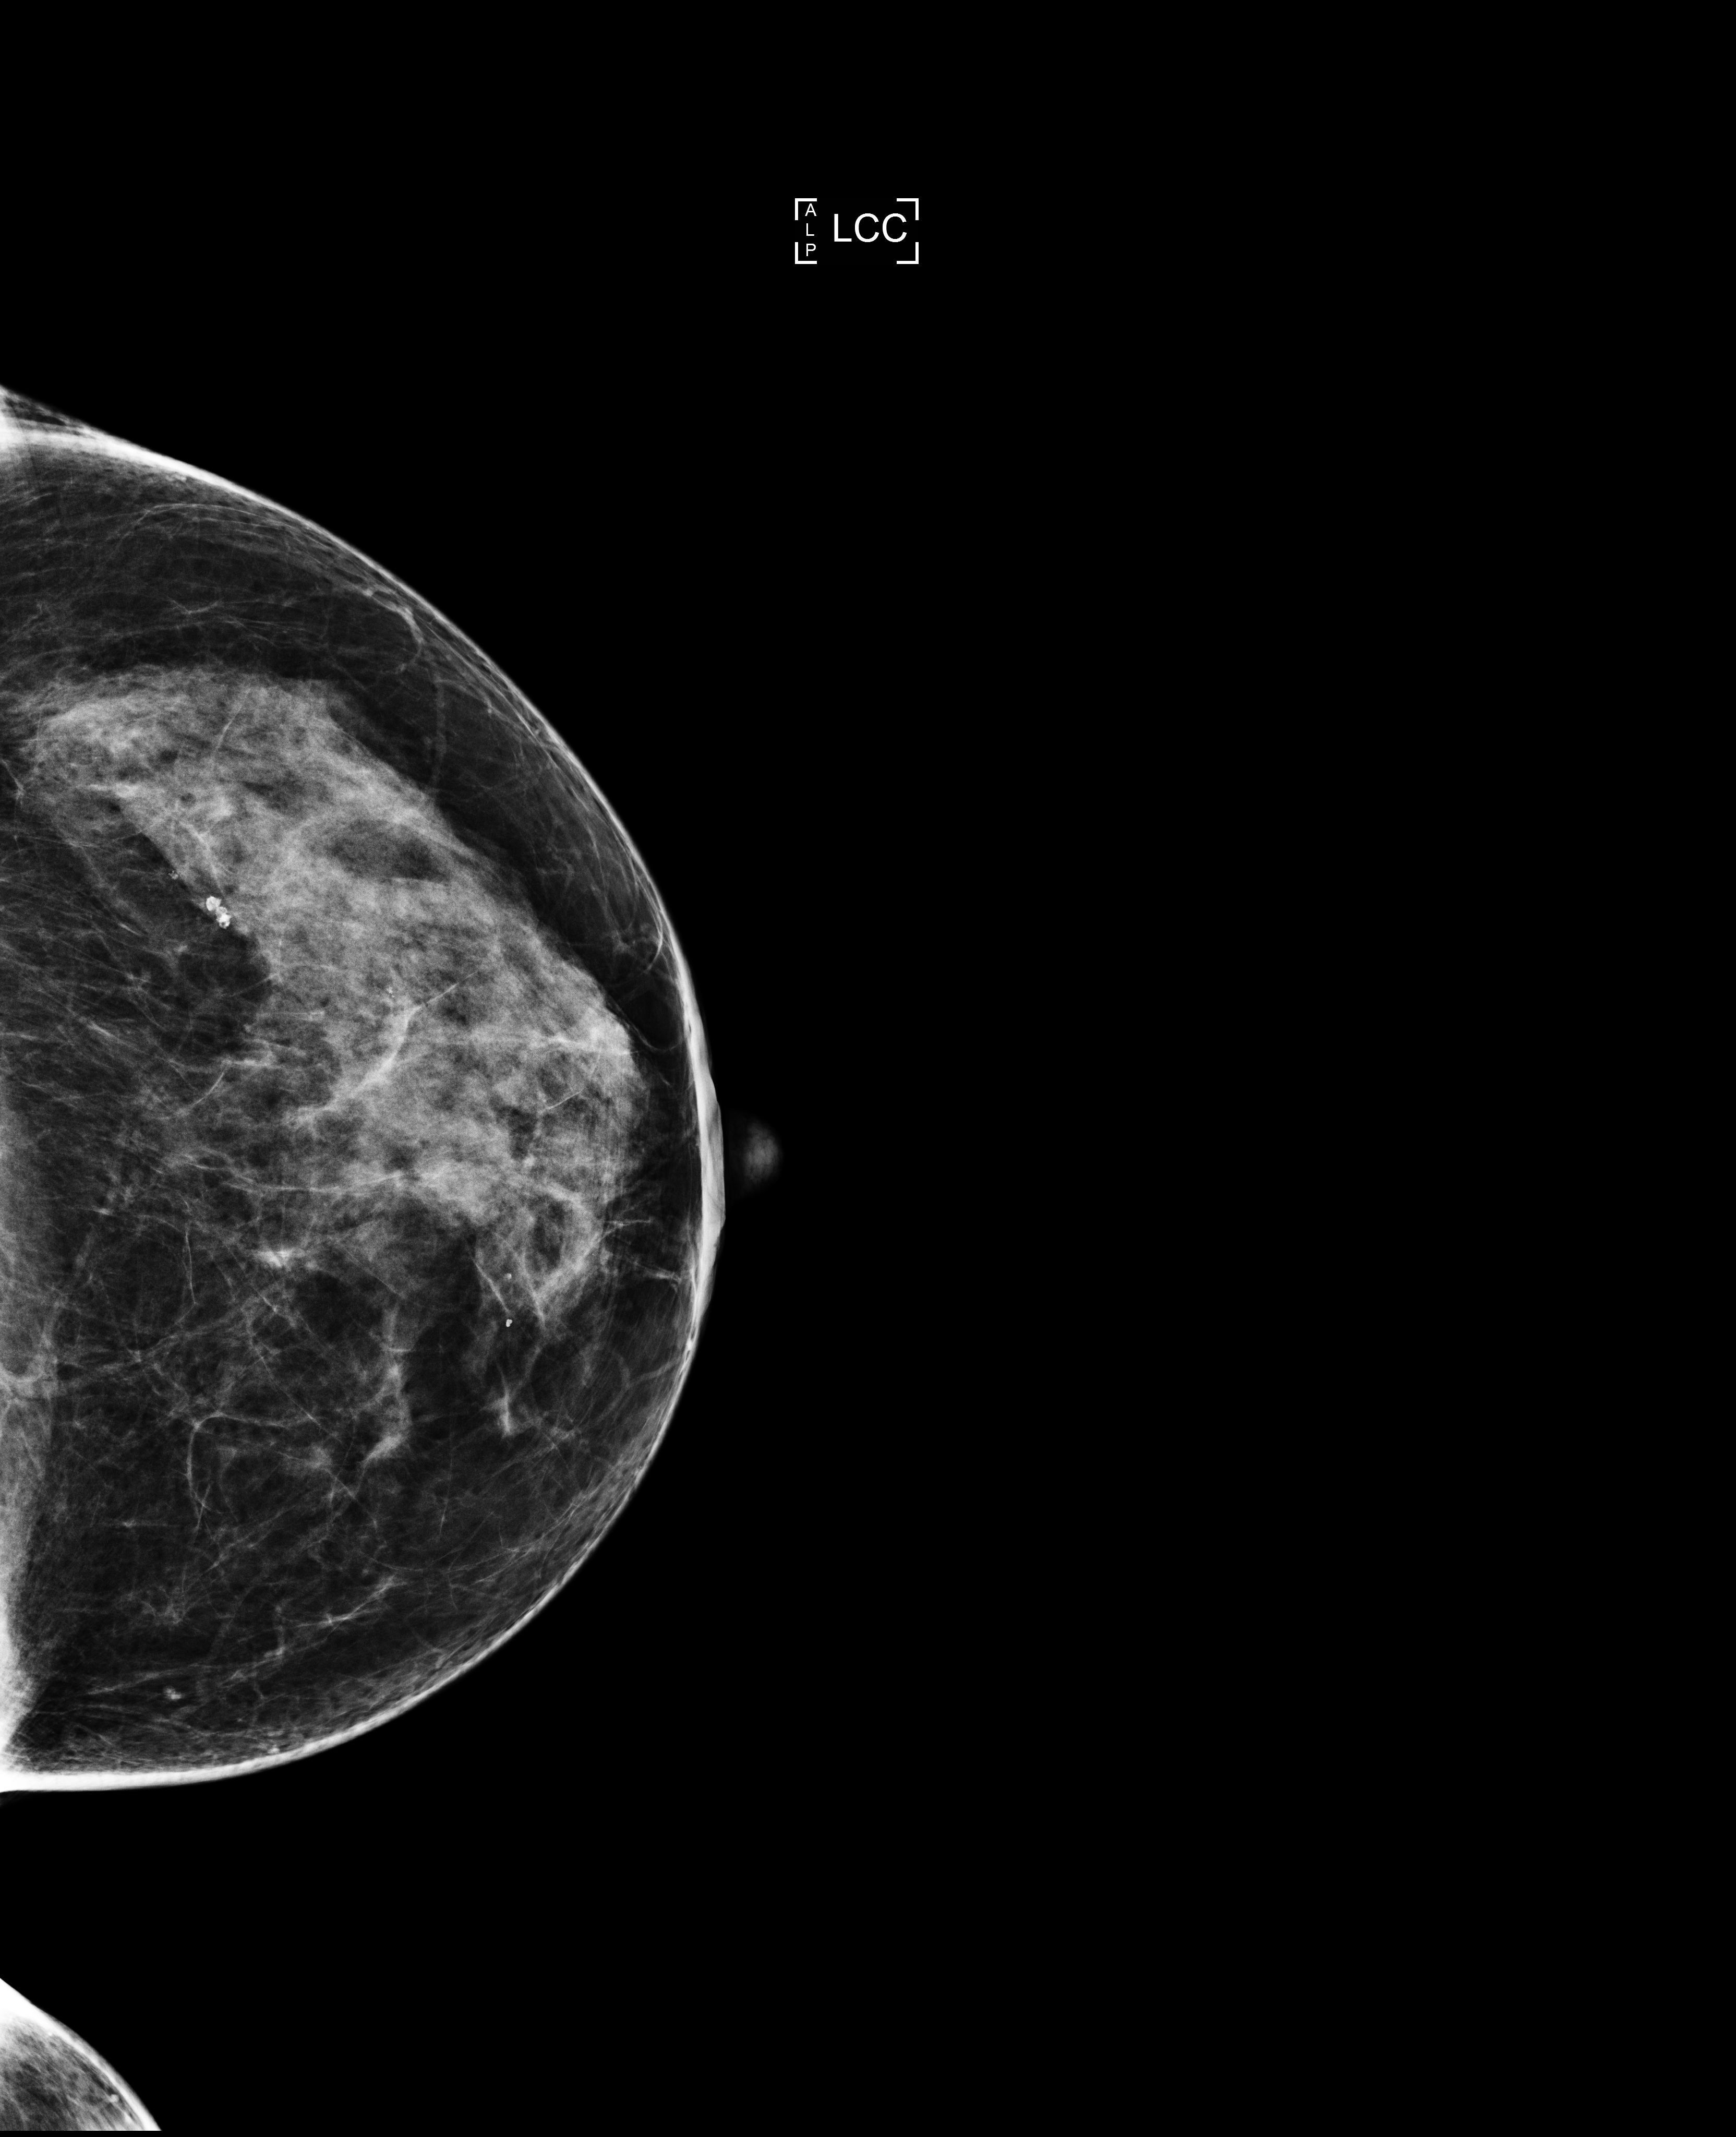
Full-field digital mammogram (FFDM); left breast; CC view; screening examination; compressed breast thickness 55 mm; system: Selenia Dimensions. Female patient, age 57 years.
- breast density at the screening exam (both breasts): heterogeneously dense (BI-RADS density category c)
- final BI-RADS category for the screening round (tomosynthesis exam, both breasts): category 1
- recall: no recall after this screen